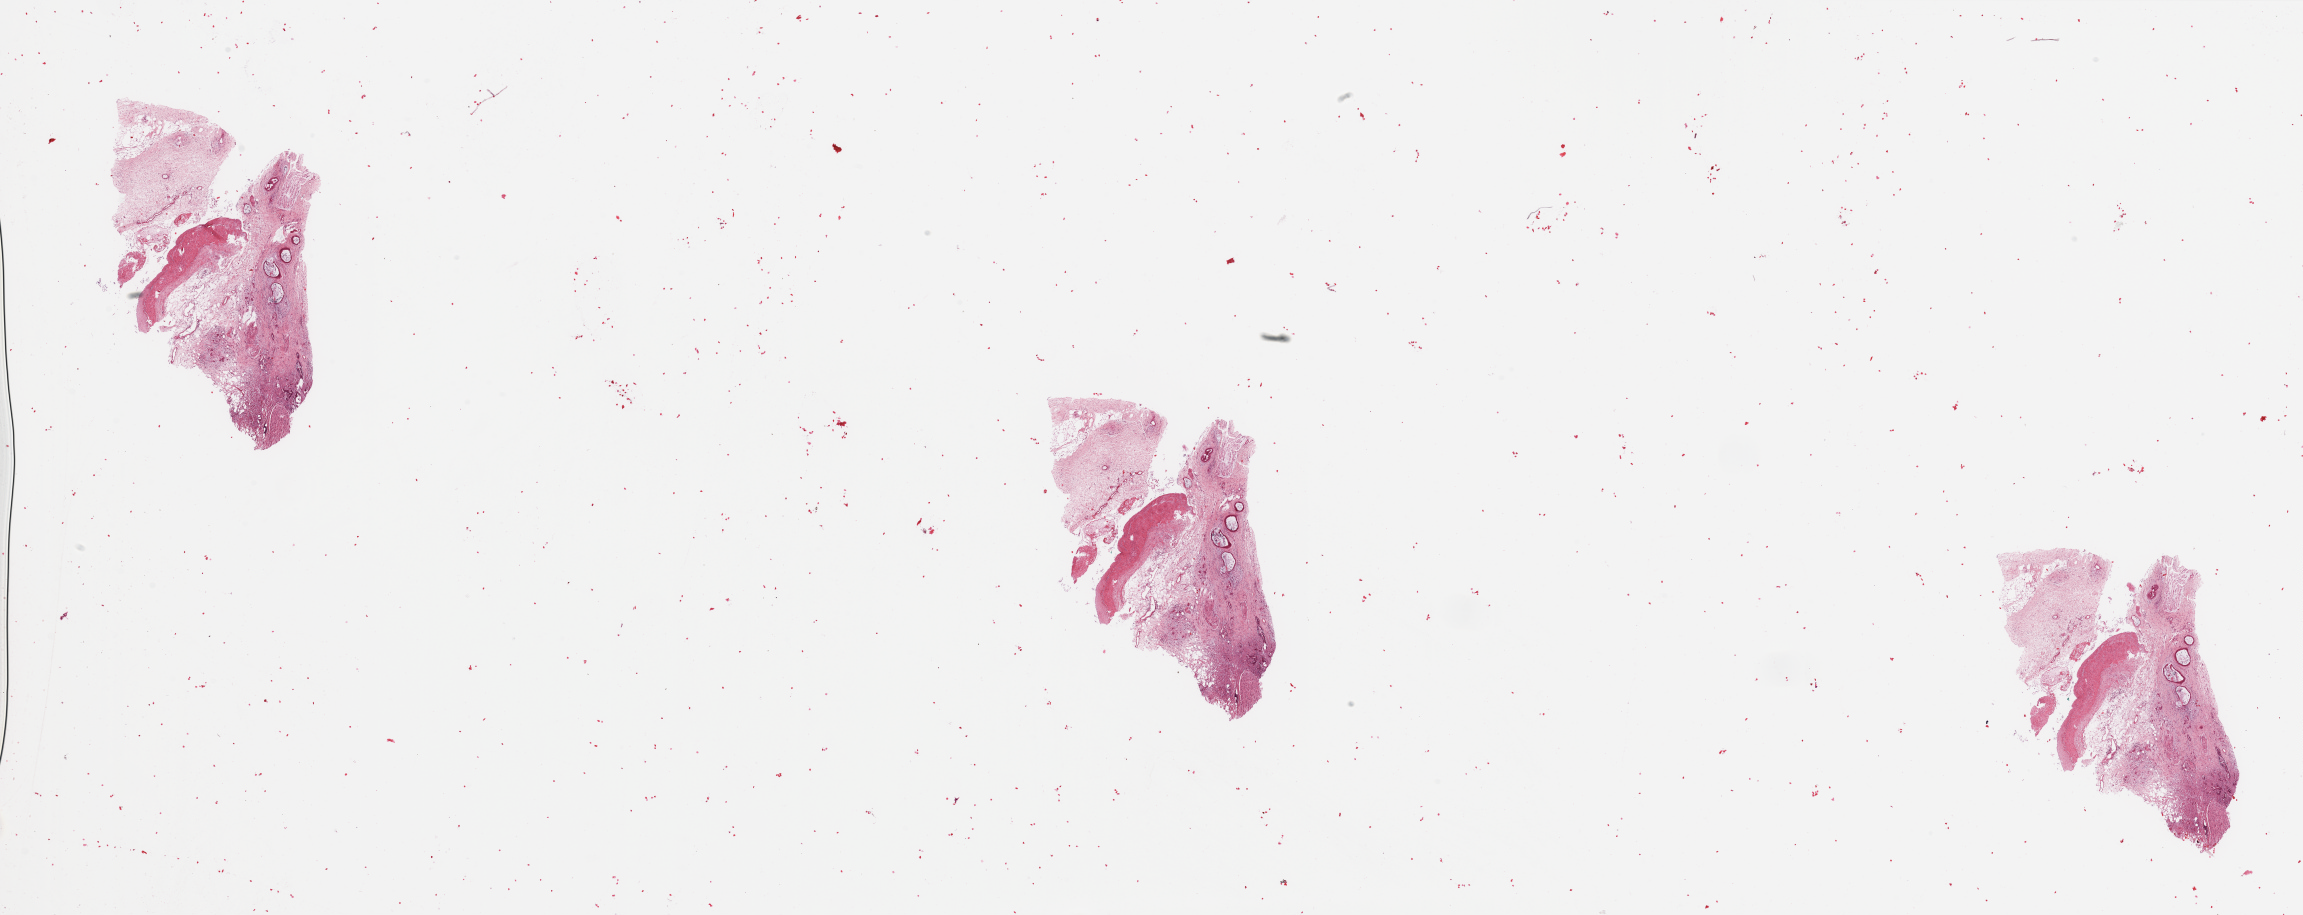
Hematoxylin and eosin (H&E) stained whole-slide image — a low-resolution overview of the entire scanned area, about 36.4 x 14.5 mm, tumour tissue sample, sampled site: pancreas. Patient: female, age 64 years. Histologic grade: G2 (moderately differentiated). Slide review estimates, as recorded: tumour nuclei 20%, necrosis 0%.
• histologic diagnosis: Infiltrating duct carcinoma, NOS
• AJCC pathologic stage: III
• primary tumour site (as recorded): head